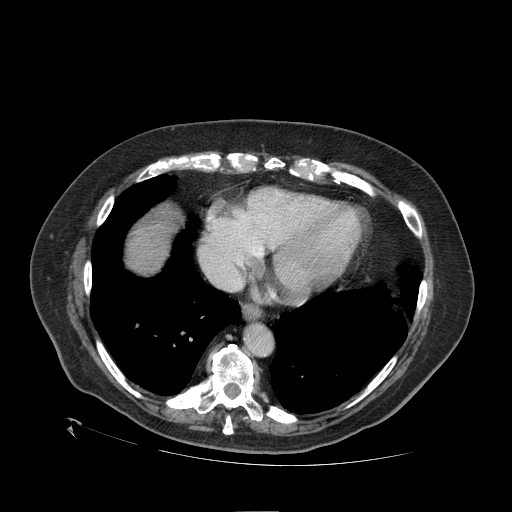
Contrast-enhanced abdominal CT (liver protocol), one axial slice. Position 99 of 109 along the scan axis. Reconstruction kernel STANDARD. 120 kVp. One of 2 acquisitions stored at this slice position. Soft-tissue window (W 400 / L 40 HU). 2.5 mm slice thickness. 512 × 512 image matrix, field of view 460 × 460 mm. From the clinical record (not read from this slice): diagnosis: hepatocellular carcinoma (patient treated with transarterial chemoembolisation; whether this scan precedes or follows treatment is not stated here); TNM stage (as recorded): Stage-I; Child-Pugh class: A; tumour differentiation: no biopsy; tumour nodularity: uninodular.
Annotated regions visible in this slice (semi-automatic segmentation, software-assisted and operator-edited):
- liver parenchyma outside the tumour (the mass and vessels are separate outlines, so this box may not span the whole liver): bounding box (x1, y1, x2, y2) in pixels: (126, 206, 180, 274)